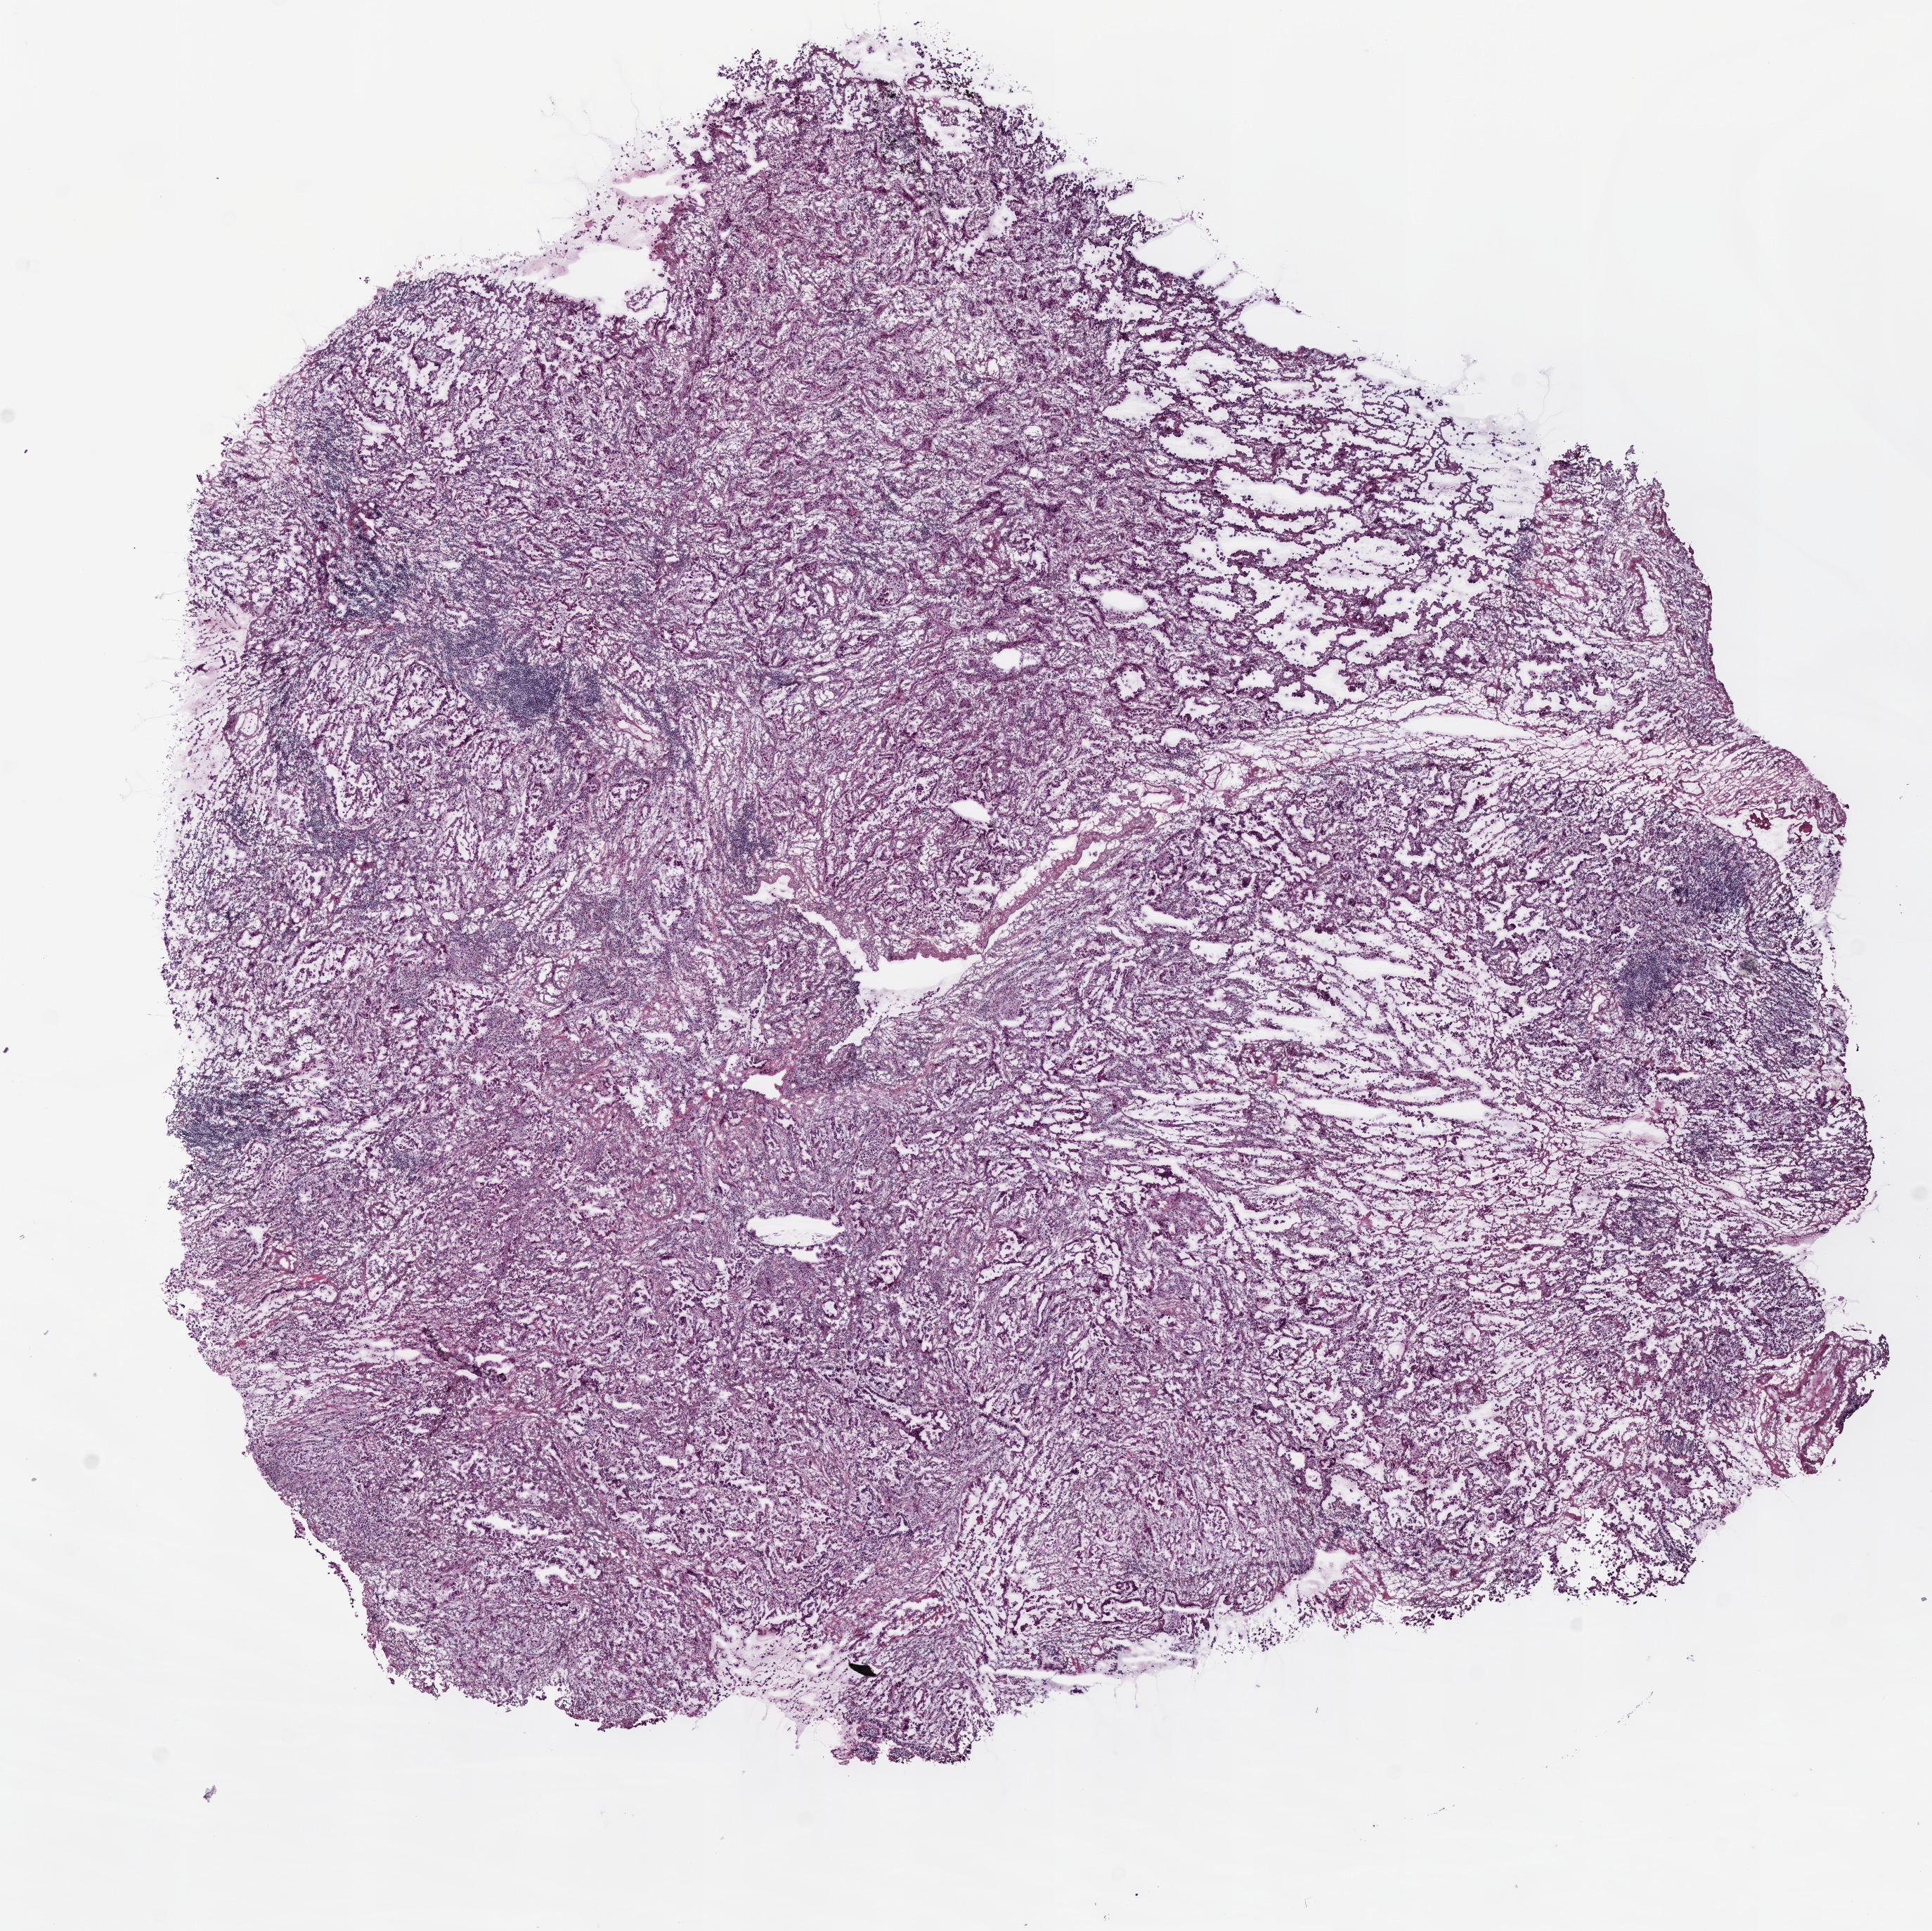
Digitized H&E tissue section (whole slide), low-resolution overview of the scanned area, about 11.0 x 11.0 mm (from a 20x scan); frozen section; lung, primary tumour sample. Patient: female, age at initial diagnosis 76 years.
Pathologic diagnosis: Adenocarcinoma with mixed subtypes.